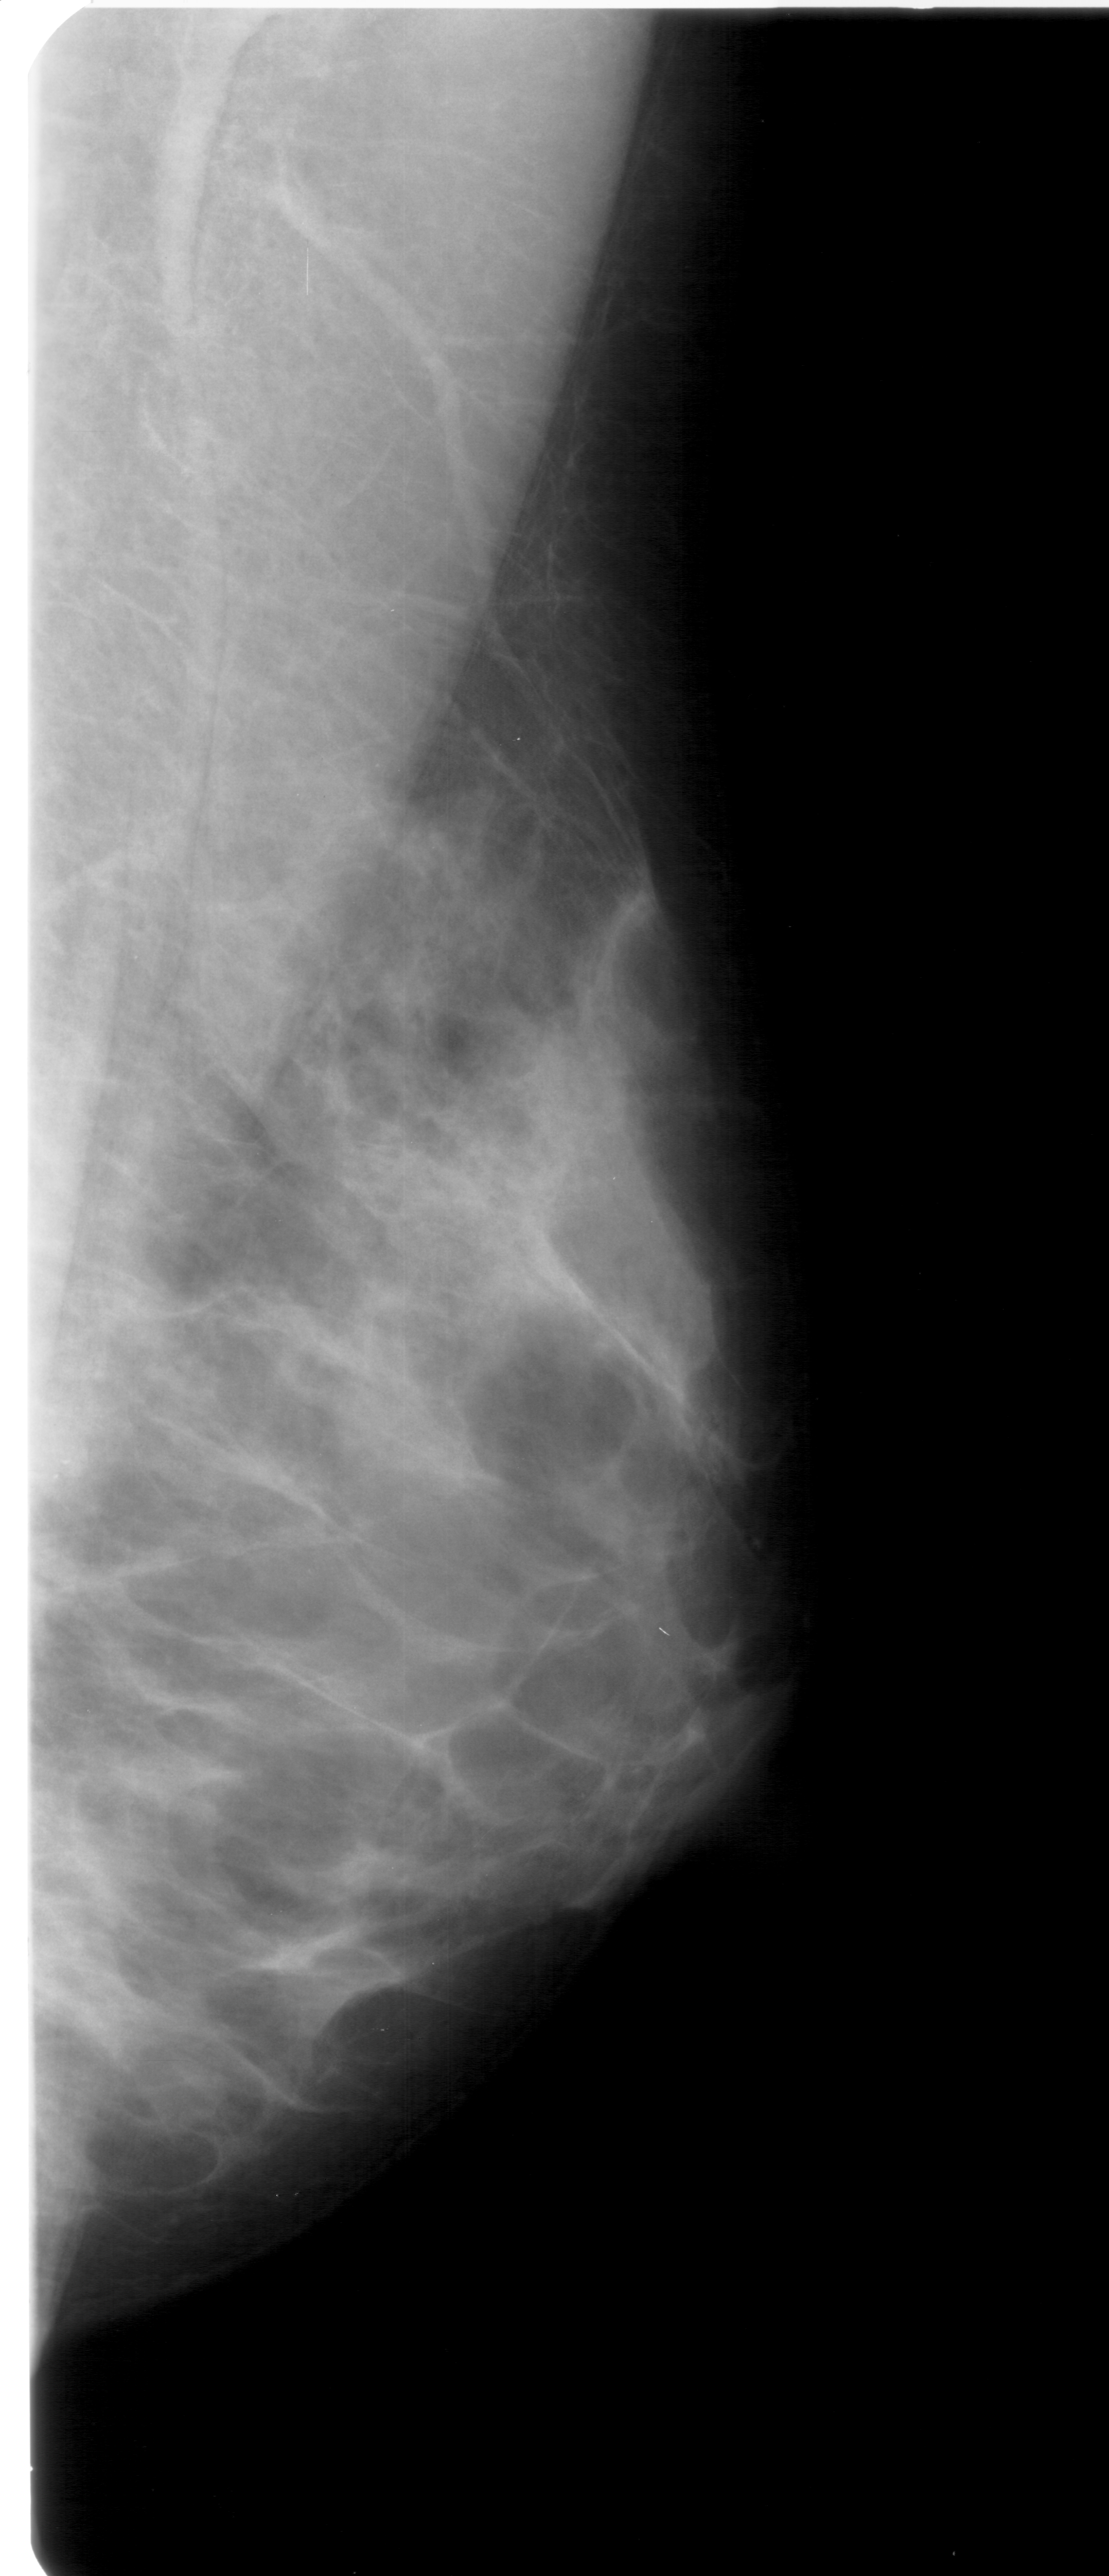
Scanned film-screen mammogram; right breast; MLO view; breast composition: extremely dense (BI-RADS density category 4 of 4).
Calcifications, morphology pleomorphic, distribution clustered; BI-RADS assessment category 4; subtlety rating 3 on a 1 (subtle) to 5 (obvious) scale; pathology result (as recorded, not read from the image): benign.